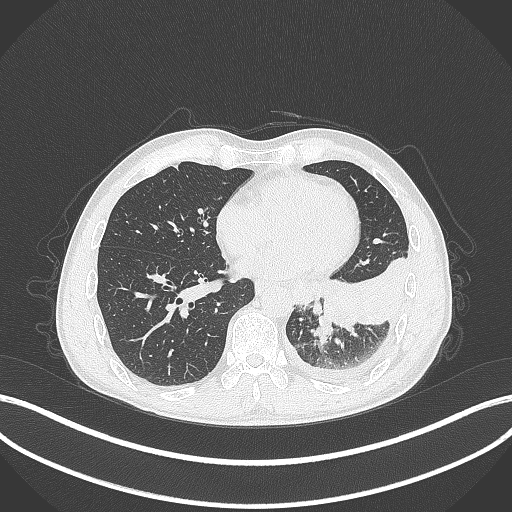
Chest CT, one axial slice. Slice 107 of 295 in the series (ordered by position). Lung window (W 1500 / L -600 HU). 1 mm slice thickness. 512 × 512 image matrix, field of view 400 × 400 mm. Male patient, age 47 years. Case-level facts recorded for this patient, not image findings: clinical TNM (as recorded): T3 N1 M1c; histopathological grade: G3.
Outlined on this slice (bounding box drawn by a radiologist):
- lung tumour (recorded histology: small cell carcinoma): box from (x=309, y=313) to (x=335, y=345) px